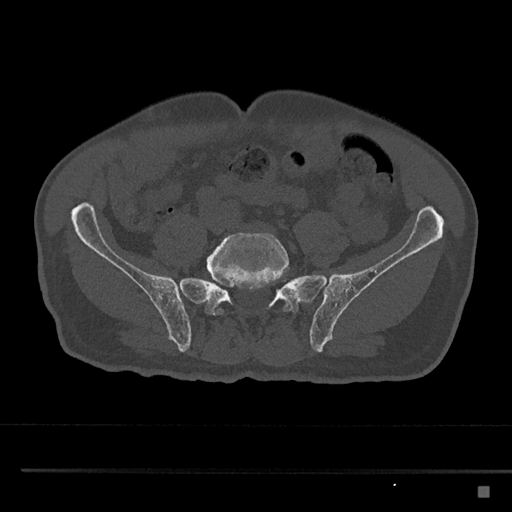
CT including the spine, one axial slice; position 558 of 797 along the scan axis; 120 kVp; bone window (W 1800 / L 400 HU); 512 × 512 image matrix. Patient: male, 59 years. From the clinical record (not read from this slice): primary cancer: prostate.
Structures marked on this image (semi-automatically segmented with operator editing):
- L5 vertebra: bounding box <206,232,291,316> (left, top, right, bottom; pixels)